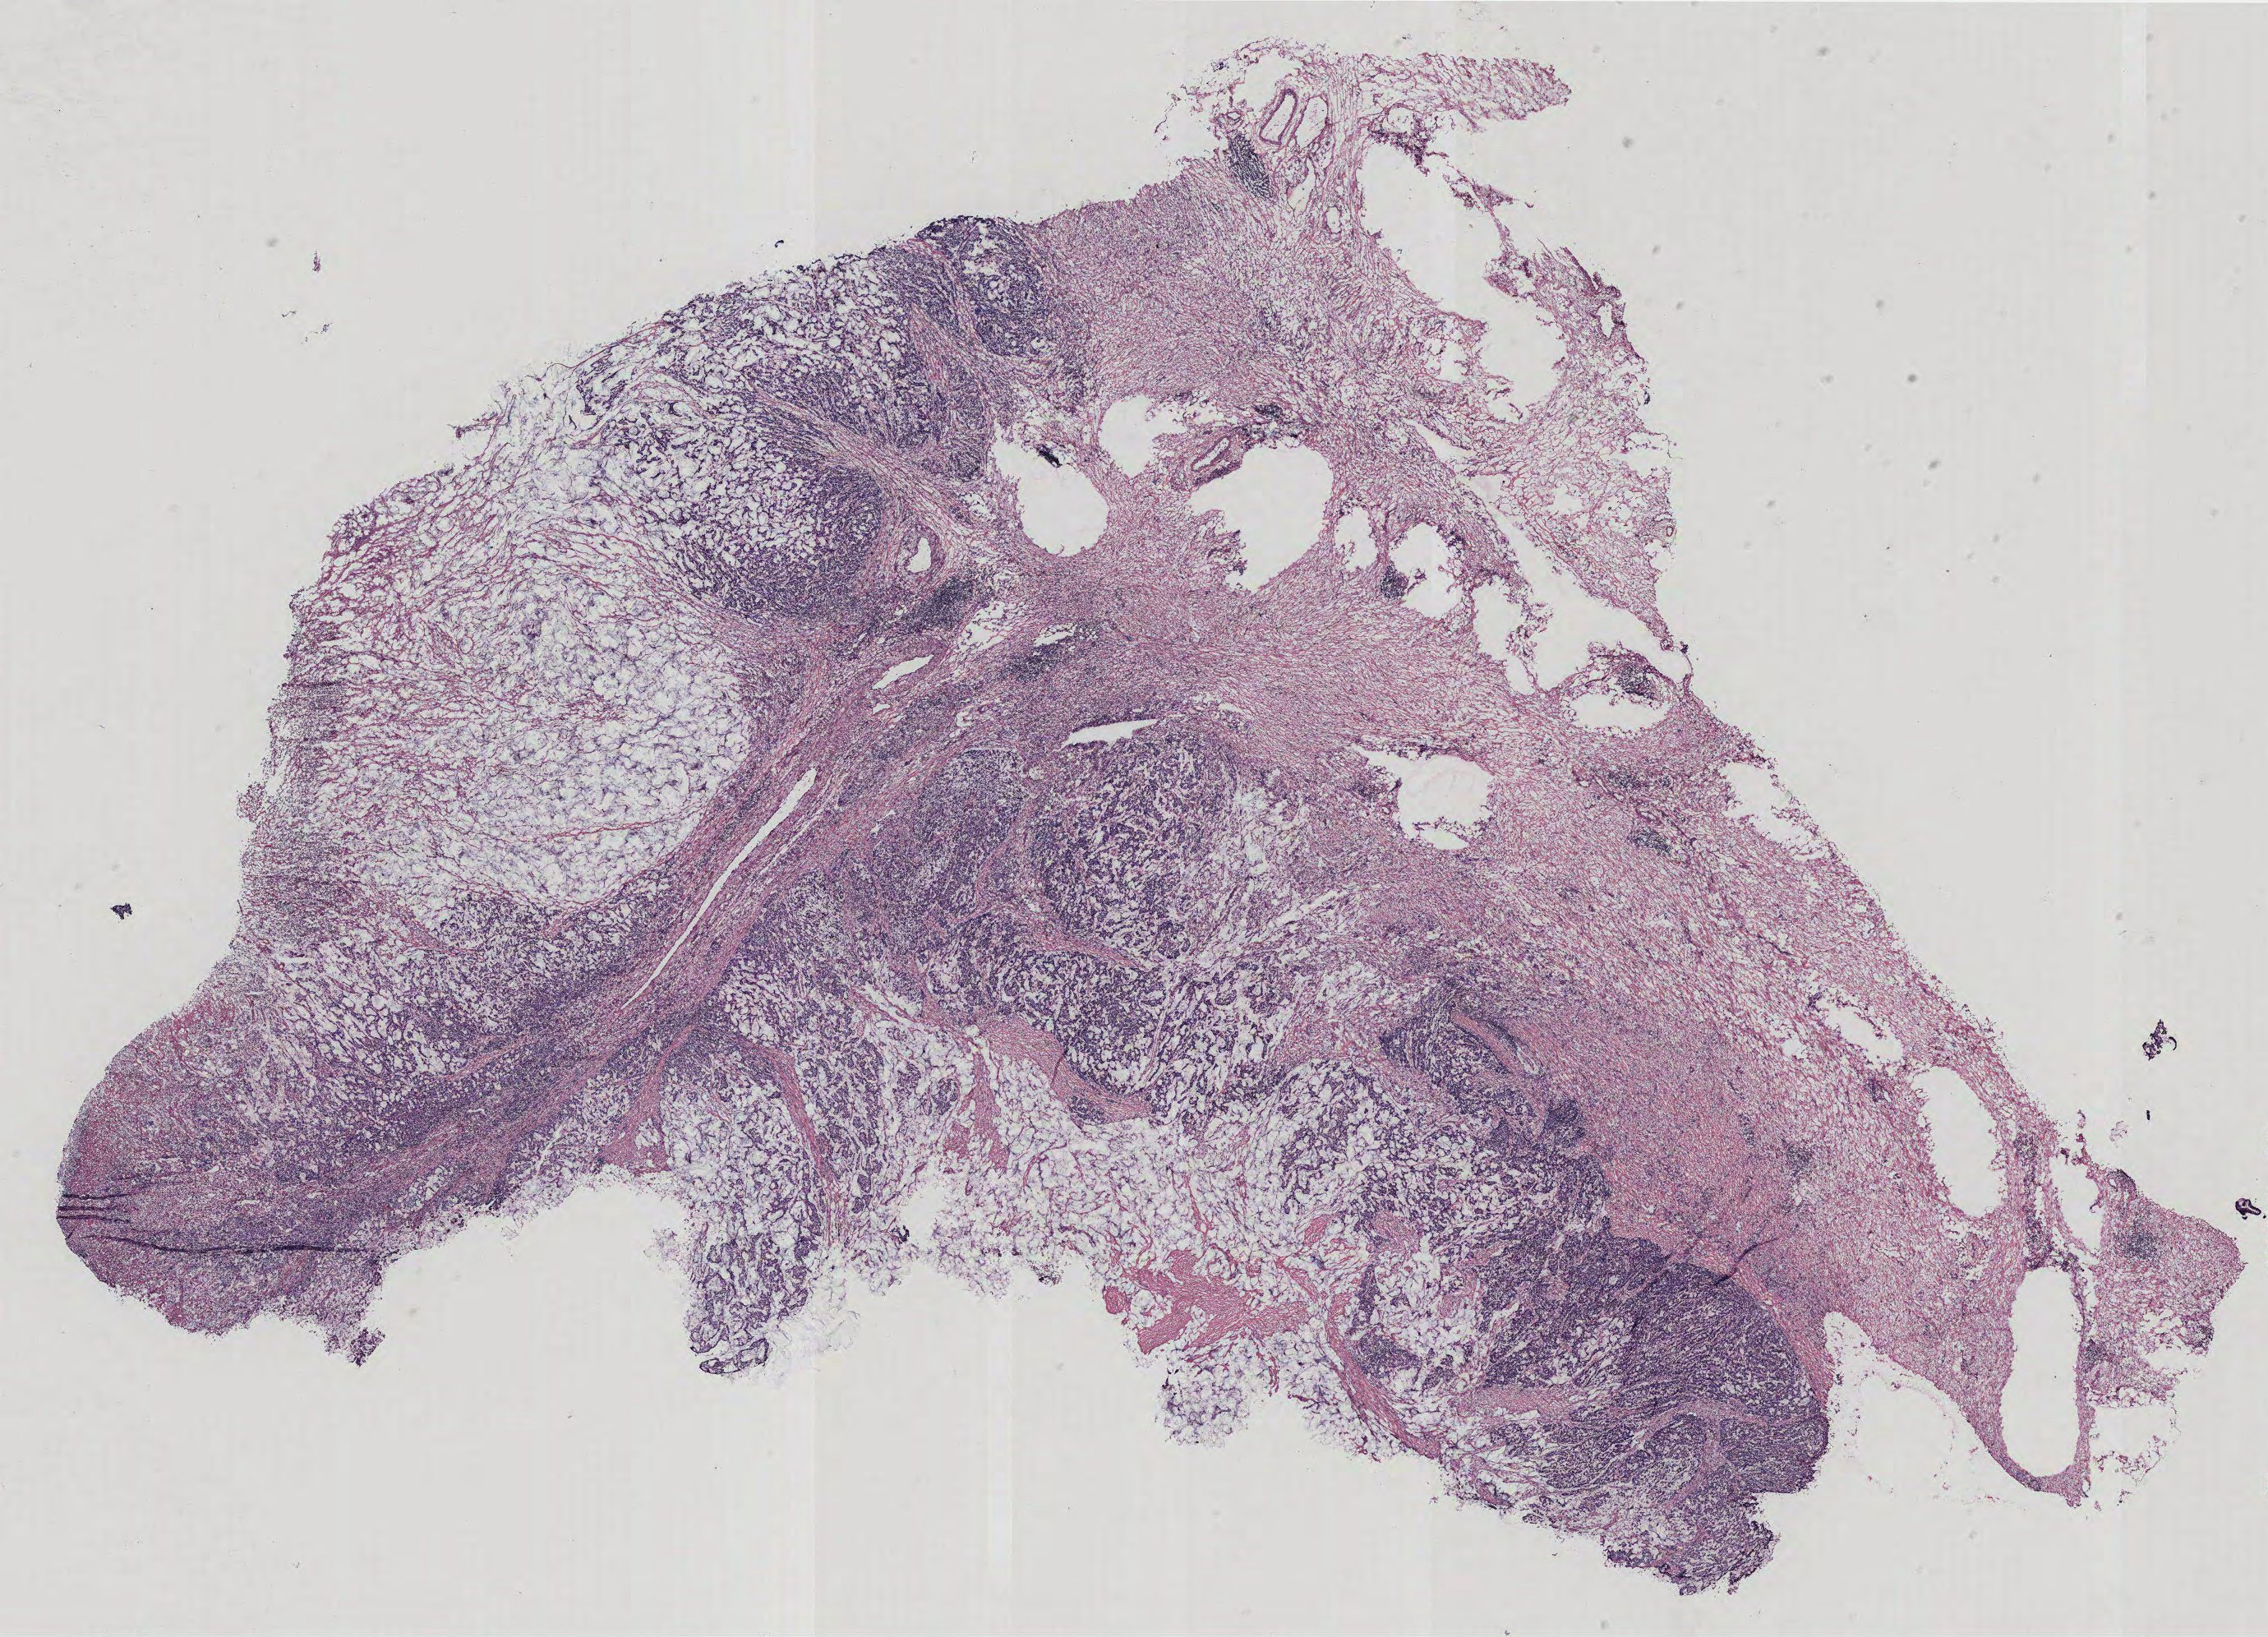
Hematoxylin and eosin (H&E) stained whole-slide image, a low-resolution overview of the entire scanned area, about 22.1 x 15.9 mm; colon, normal (non-tumour) tissue. Male, 36 y/o.
This section: normal (non-tumour) tissue from the same patient. Patient diagnosis: Adenocarcinoma, NOS.